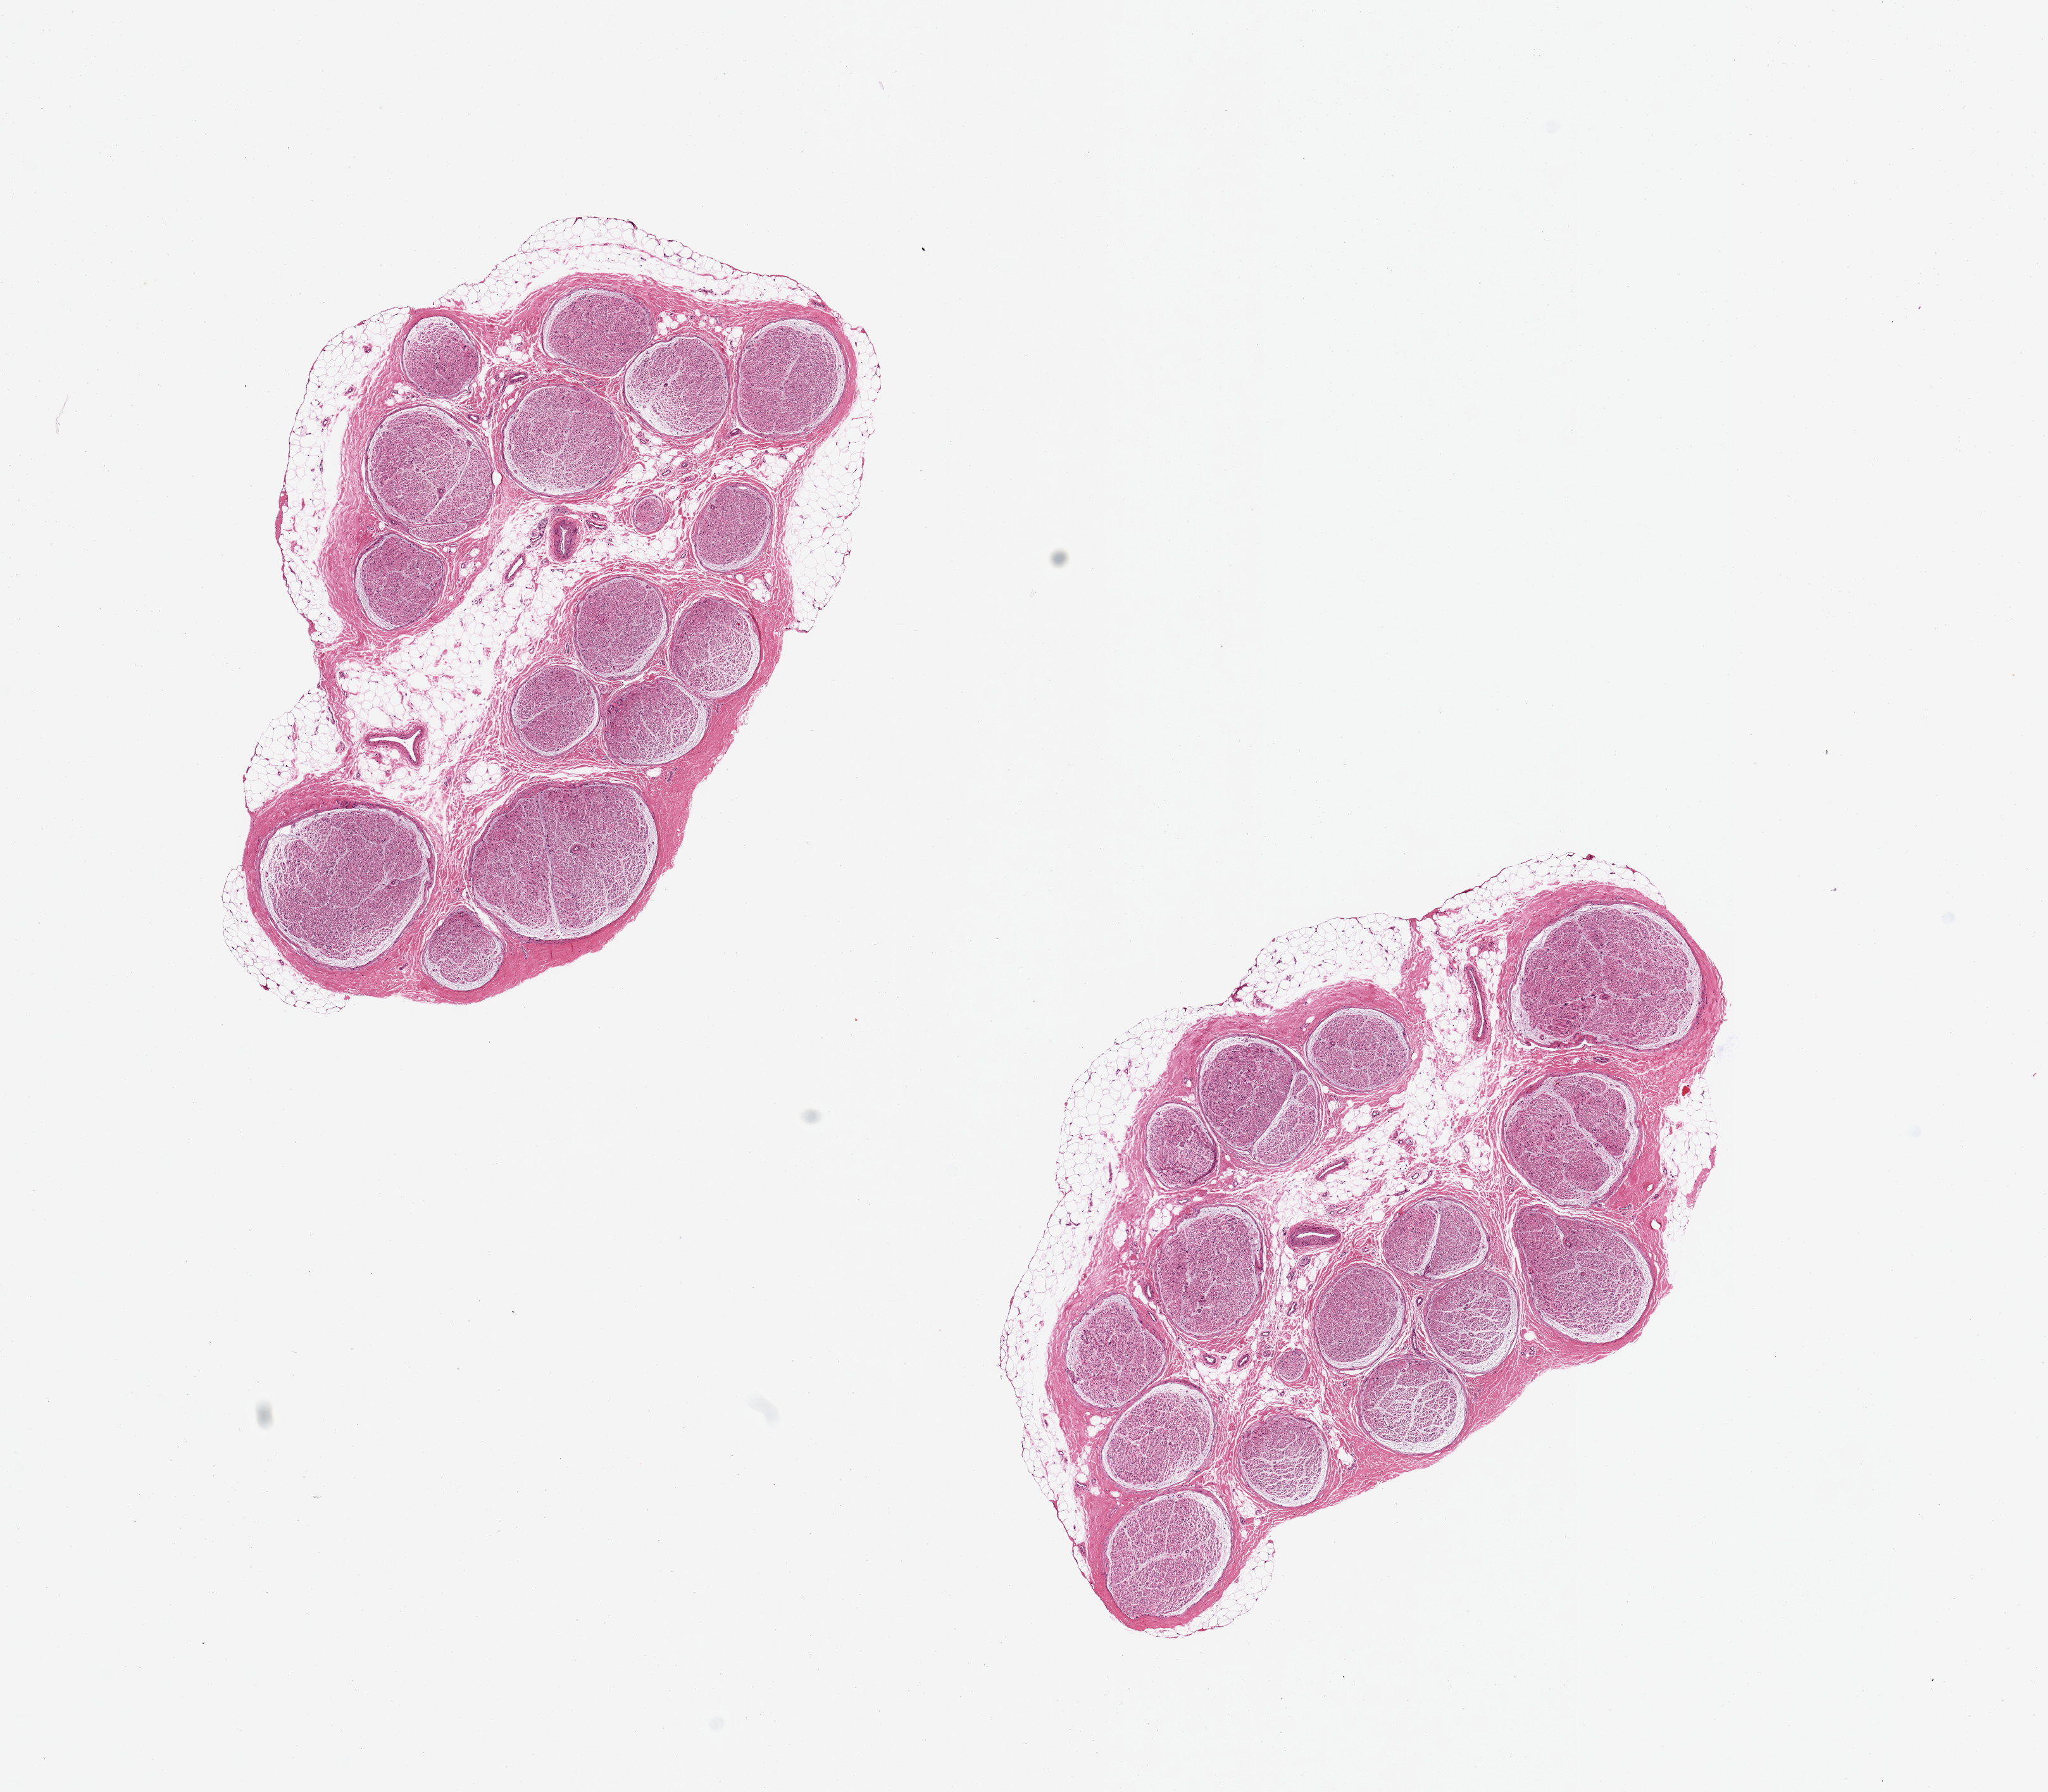
Digitized hematoxylin and eosin (H&E)-stained section, low-resolution overview of the scanned area, about 12.8 x 11.2 mm, PAXgene-fixed, paraffin-embedded tissue, section of tibial nerve (target tissue), donor tissue sample. Donor: male.
Reviewer comment on this tissue sample: 2 pieces, partial rim of trace adherent fat, up to ~0.3mm.